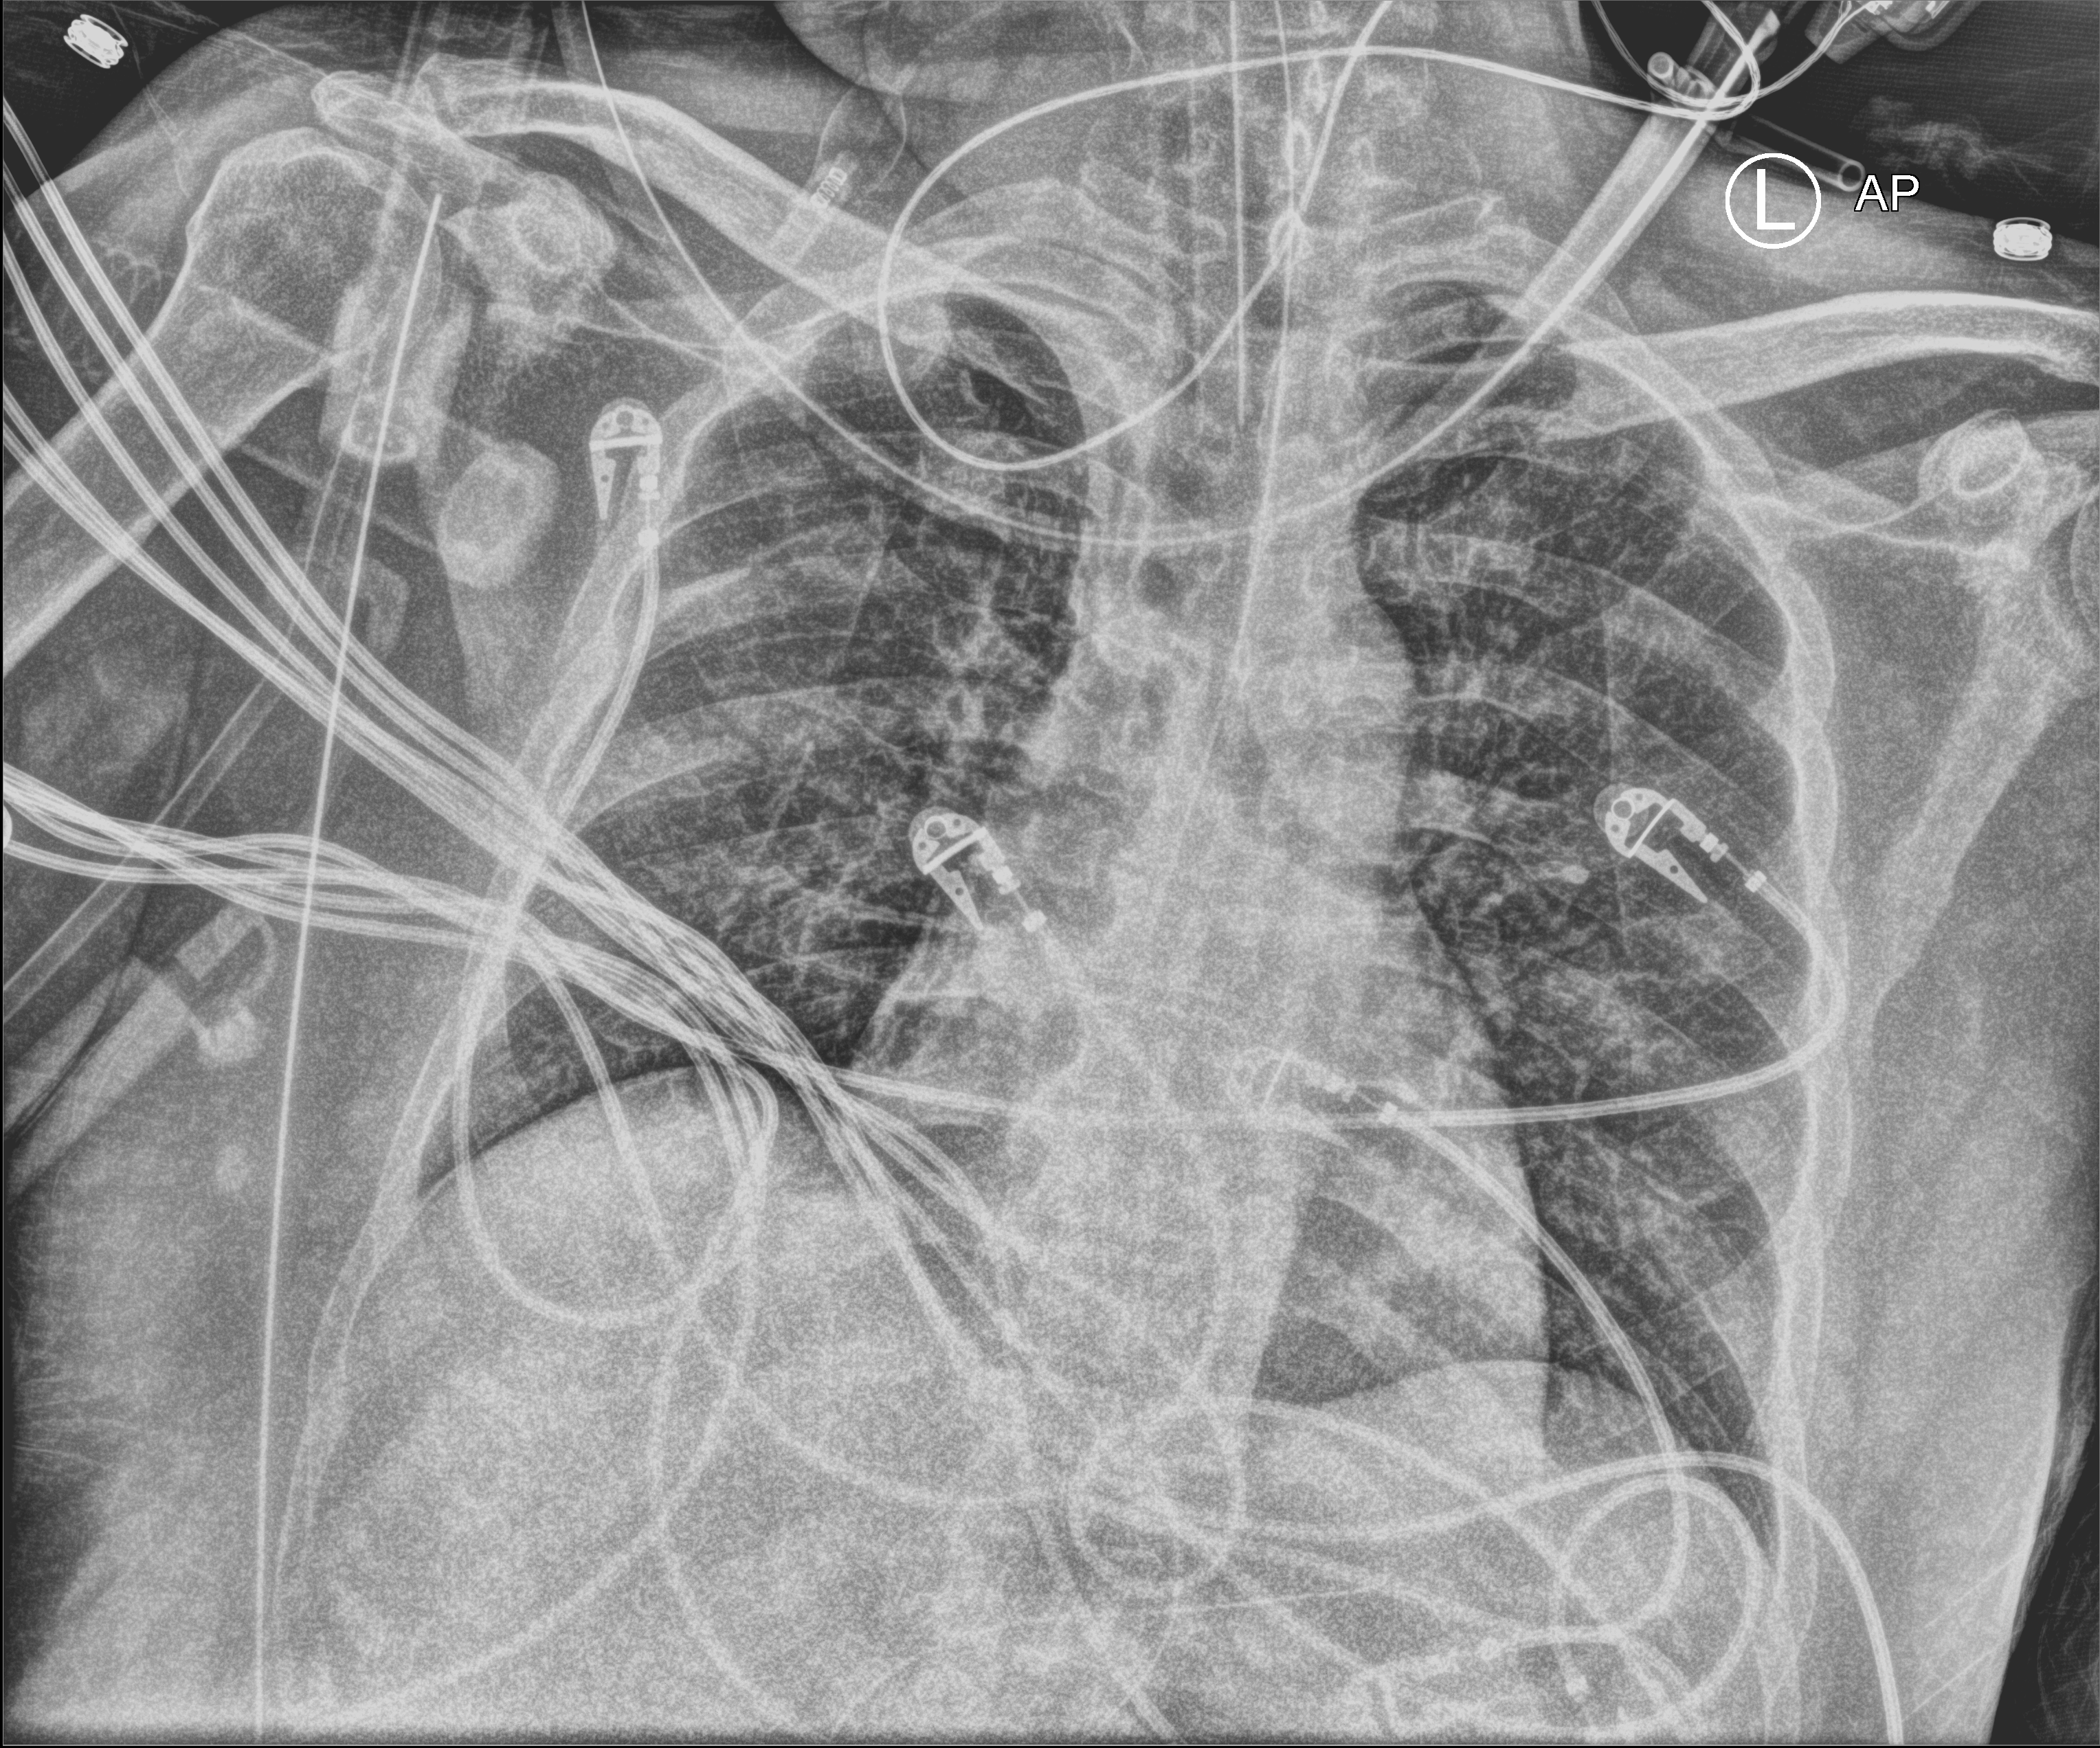
Bedside chest radiograph (computed radiography). Adult patient hospitalised with COVID-19, age 18–59 years.
Admission-level facts for this patient (not findings on this image; timing relative to this image not recorded): admitted to intensive care during this hospital stay: yes; length of hospital stay: 37 days; mechanically ventilated during this hospital stay: yes.